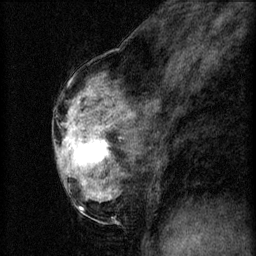
Breast MRI (dynamic contrast-enhanced), one sagittal slice. Slice 33 of 60 in the series (ordered by position). 3 images stored at this slice position (order not interpretable as contrast timing). 1.5 T. TE 4.2 ms, TR 8.2 ms. 256 × 256 image matrix. Female patient, age 56 years.
Outlined on this slice (semi-automatically segmented with operator editing):
- analysis volume of interest (the breast-tissue region the enhancement analysis was run in; not a lesion): bounding box <60,124,112,179> (left, top, right, bottom; pixels)
- tumour enhancement mask (voxels above the 70 % enhancement threshold inside the analysis volume of interest): <64,126,108,163>